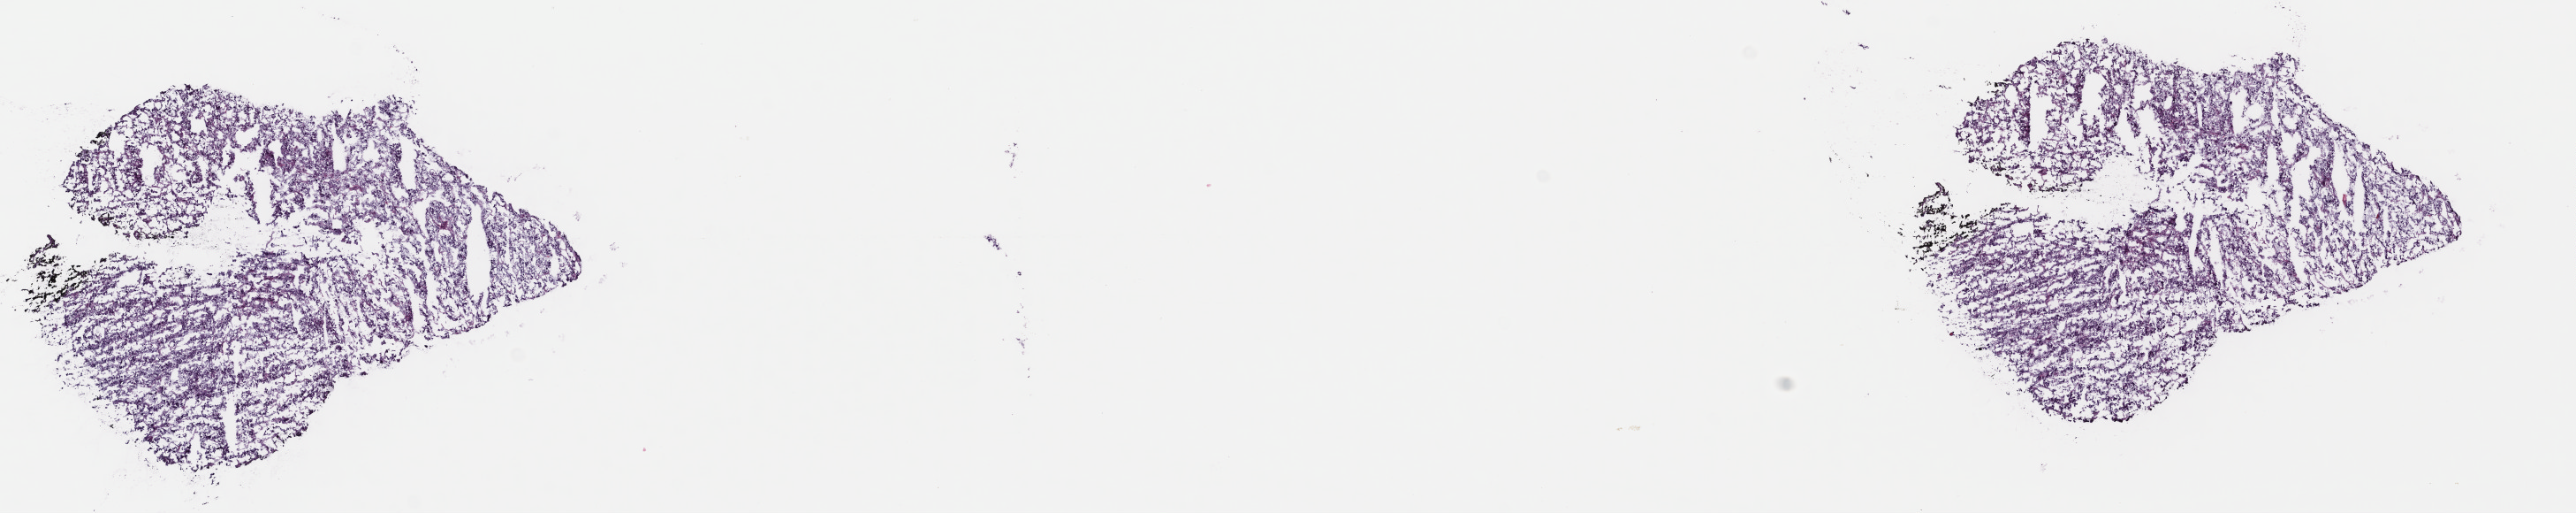
Whole-slide histology image, Hematoxylin and eosin (H&E) stained — a low-resolution overview of the entire scanned area, about 22.9 x 4.6 mm (from a 40x scan), frozen section from the top of the tissue portion, sample: primary tumour, adrenal gland. Patient: male, age at initial diagnosis 58 years. Composition of this section per pathologist review: tumour cells 99%, tumour nuclei 99%, normal cells 0%, stromal cells 1%, necrosis 0%. Infiltration values recorded for this section: lymphocyte infiltration 0%, monocyte infiltration 0%, neutrophil infiltration 0%.
- pathologic diagnosis: Pheochromocytoma, NOS